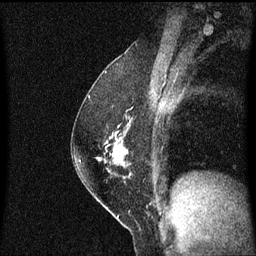
Breast MRI (dynamic contrast-enhanced), one sagittal slice. Slice 35 of 60 in the series (ordered by position). Dynamic contrast-enhanced series, image 2 of 3 at this slice position (ordered by acquisition). 1.5 T. TE 4.2 ms, TR 8.4 ms. 2 mm slice thickness. 256 × 256 image matrix, field of view 200 × 200 mm. Female patient, age 52 years. Case-level facts recorded for this patient, not image findings: setting: breast cancer imaged before/during neoadjuvant chemotherapy; receptor status: HER2-positive.
Outlined on this slice (semi-automatically segmented with operator editing):
- analysis volume of interest (the breast-tissue region the enhancement analysis was run in; not a lesion): bounding box [x1, y1, x2, y2] px = [73, 118, 134, 187]
- tumour enhancement mask (voxels above the 70 % enhancement threshold inside the analysis volume of interest): [110, 138, 127, 155]